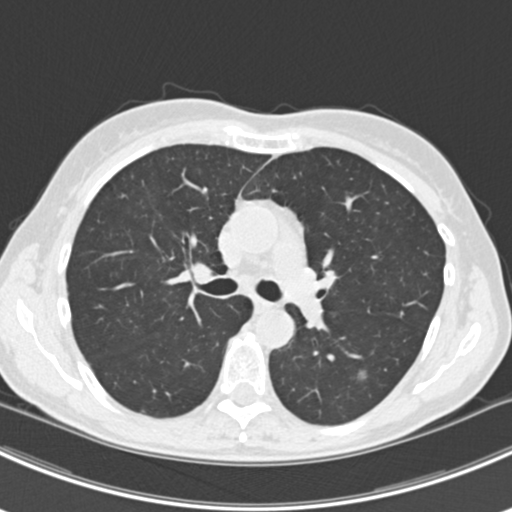
Low-dose screening chest CT, axial slice. Baseline annual screen. Lung window (W 1500 / L -600 HU). 2 mm slice thickness. Standard (soft-tissue) reconstruction kernel (B30f). Slice 71 of 224 in the series. Female, age 63 years at enrolment. Current smoker at enrolment.
• Expert reader's lesion annotation, box from (x=342, y=362) to (x=379, y=392) px.
• The screening reader recorded 10 non-calcified nodules or masses ≥4 mm on this exam (right lower lobe, right lower lobe, left lower lobe, left lower lobe, right middle lobe, right lower lobe, left lower lobe, left upper lobe, right upper lobe, left upper lobe); which of them this box marks is not recorded.
• Official screen result: positive, change unspecified: nodule(s) >= 4 mm or enlarging nodule(s), mass(es), or other non-specific abnormalities suspicious for lung cancer.
• Participant outcome: lung cancer diagnosed 751 days after this screen — bronchiolo-alveolar adenocarcinoma, NOS, right upper lobe, right middle lobe, right lower lobe, left upper lobe, left lower lobe, moderately differentiated (G2), stage IV (AJCC 6th edition).